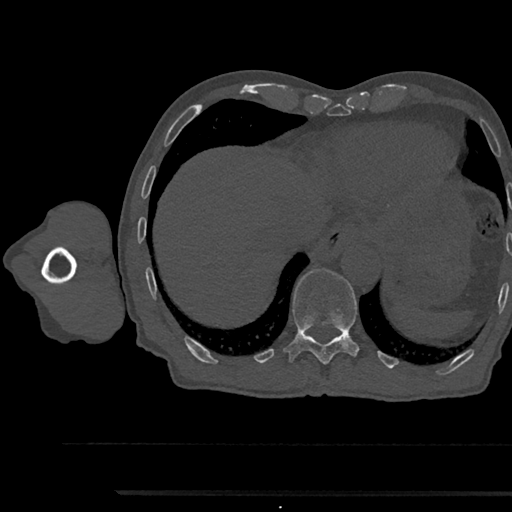
CT including the spine, one axial slice; slice 787 of 797 in the series (ordered by position); reconstruction kernel Br40s/3; 120 kVp; bone window (W 1800 / L 400 HU); 512 × 512 image matrix, field of view 367 × 367 mm. Male patient, age 79 years. Case-level facts recorded for this patient, not image findings: primary cancer: prostate.
Annotated regions visible in this slice (semi-automatic segmentation, software-assisted and operator-edited):
- T11 vertebra: bounding box [x1, y1, x2, y2] px = [284, 268, 359, 365]